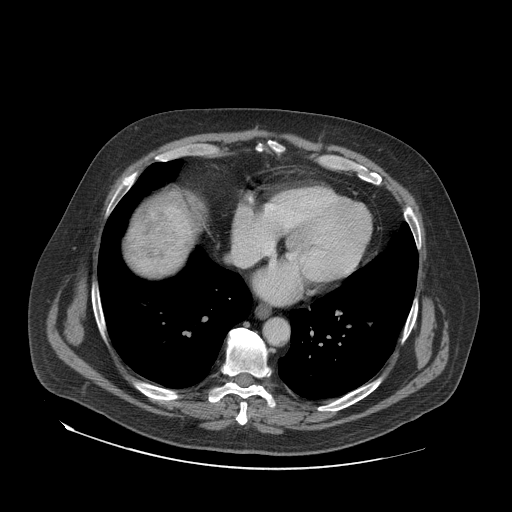
Contrast-enhanced abdominal CT (liver protocol), one axial slice. Position 73 of 79 along the scan axis. Reconstruction kernel STANDARD. 140 kVp. Soft-tissue window (W 400 / L 40 HU). 2.5 mm slice thickness. 512 × 512 image matrix, field of view 480 × 480 mm. Case-level facts recorded for this patient, not image findings: diagnosis: hepatocellular carcinoma (patient treated with transarterial chemoembolisation; whether this scan precedes or follows treatment is not stated here); TNM stage (as recorded): Stage-IVA; Child-Pugh class: A; tumour nodularity: multinodular.
Annotated regions visible in this slice (semi-automatically segmented with operator editing):
- liver parenchyma outside the tumour (the mass and vessels are separate outlines, so this box may not span the whole liver): bounding box (x1, y1, x2, y2) in pixels: (128, 200, 194, 274)
- mass: (128, 204, 191, 274)